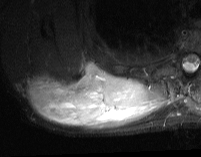
MRI of an extremity soft-tissue mass, one axial slice. STIR. MR volume resampled by the dataset authors to the PET/CT grid (not the native acquisition matrix). 201 × 157 image matrix, field of view 196 × 153 mm. Male patient. From the clinical record (not read from this slice): histological type: pleiomorphic spindle cell undifferentiated; grade: high; site of the primary tumour: right parascapusular.
Outlined on this slice (expert contour drawn on MRI and transferred to this co-registered scan by the dataset authors):
- gross tumour volume including surrounding oedema: bounding box (x1, y1, x2, y2) in pixels: (28, 61, 168, 129)
- gross tumour volume (mass): (28, 62, 148, 126)